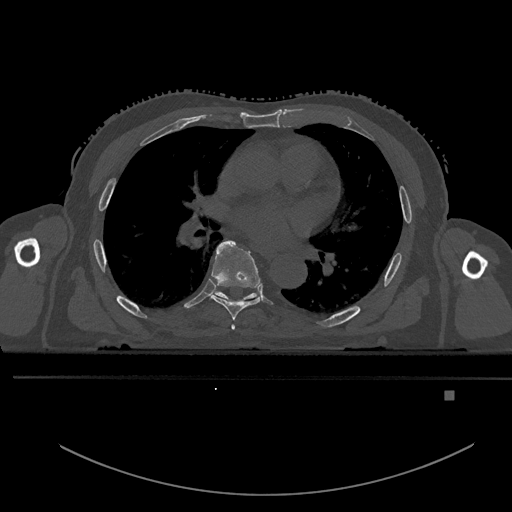
CT including the spine, one axial slice. Slice 292 of 969 in the series (ordered by position). Bone window (W 1800 / L 400 HU). 0.5 mm slice thickness. 512 × 512 image matrix, field of view 456 × 456 mm. Male patient, age 82 years. From the clinical record (not read from this slice): primary cancer: prostate.
Annotated regions visible in this slice (semi-automatic segmentation, software-assisted and operator-edited):
- T5 vertebra: bounding box (x1, y1, x2, y2) in pixels: (231, 325, 235, 331)
- T6 vertebra: (210, 240, 261, 320)
- T7 vertebra: (214, 291, 256, 299)